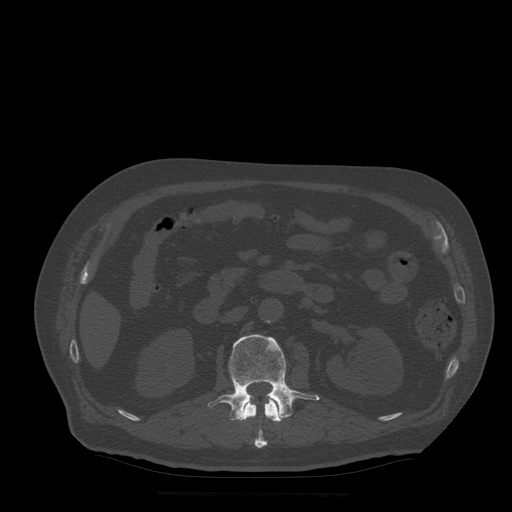
CT including the spine, one axial slice. Slice 176 of 522 in the series (ordered by position). Bone window (W 1800 / L 400 HU). 1.25 mm slice thickness. 512 × 512 image matrix, field of view 420 × 420 mm. Patient age 72 years. Case-level facts recorded for this patient, not image findings: primary cancer: prostate.
Annotated regions visible in this slice (semi-automatic segmentation, software-assisted and operator-edited):
- L1 vertebra: box from (x=242, y=396) to (x=281, y=449) px
- L2 vertebra: (x=208, y=335)–(x=320, y=421)